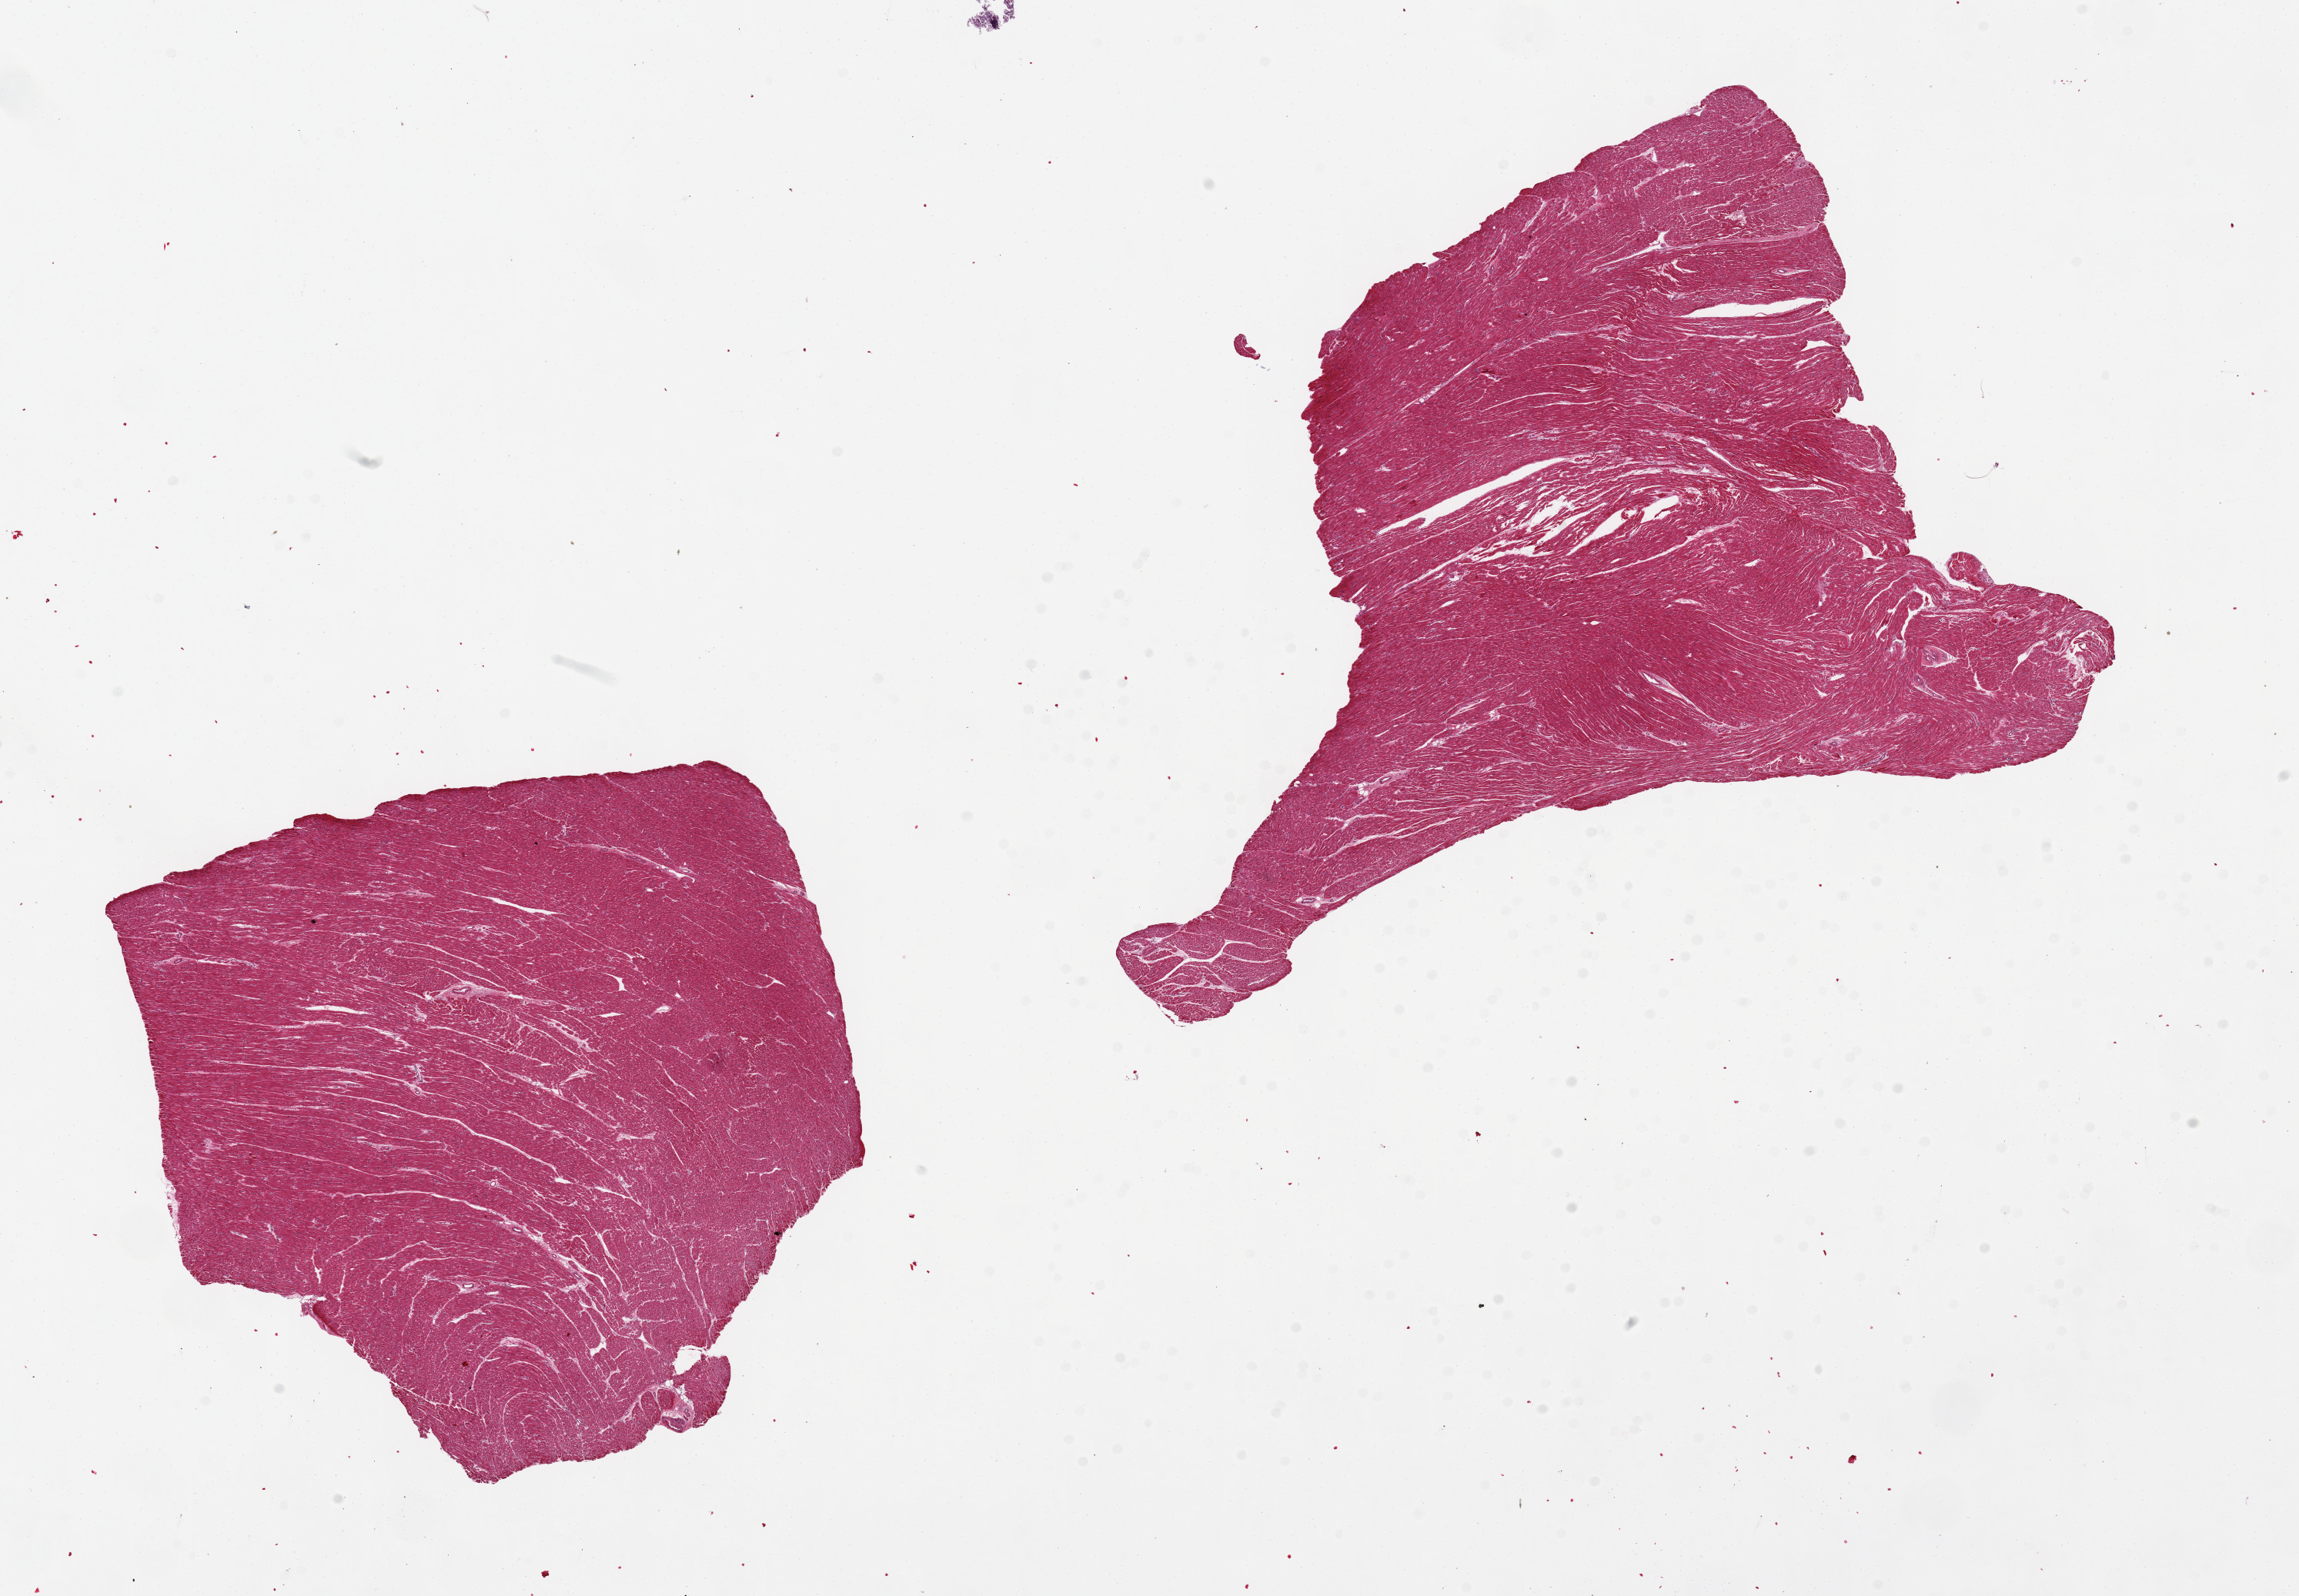
Hematoxylin and eosin (H&E) whole-slide image, brightfield — a low-resolution overview of the entire scanned area, about 23.6 x 16.4 mm (from a 20x scan); PAXgene-fixed, paraffin-embedded tissue; target tissue: heart; tissue donor sample. Donor sex: female.
Reviewer comment on this tissue sample: 2 pieces. 8x8 & 11x8mm; No extraneous fat.